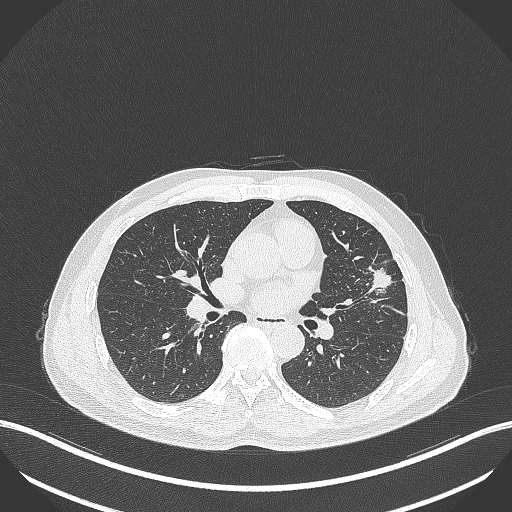
Chest CT, one axial slice. Position 207 of 418 along the scan axis. Reconstruction kernel B70f. 120 kVp. Lung window (W 1500 / L -600 HU). 512 × 512 image matrix. Patient: male, 55 years. From the clinical record (not read from this slice): clinical TNM (as recorded): T1c N0 M0.
Outlined on this slice (bounding box drawn by a radiologist):
- lung tumour (recorded histology: adenocarcinoma): bounding box <363,262,399,292> (left, top, right, bottom; pixels)